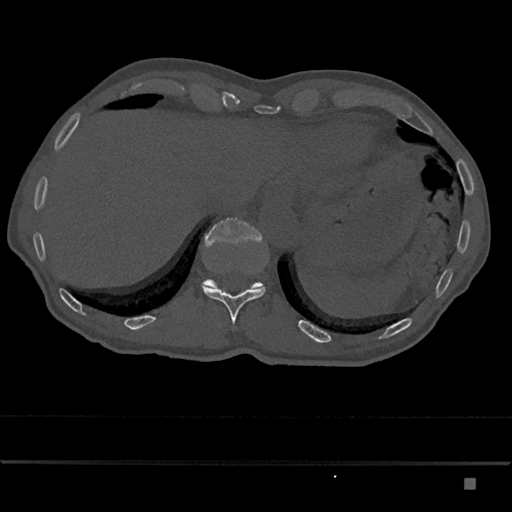
CT including the spine, one axial slice. Slice 660 of 797 in the series (ordered by position). Reconstruction kernel Br40s/3. 120 kVp. Bone window (W 1800 / L 400 HU). 0.5 mm slice thickness. 512 × 512 image matrix, field of view 390 × 390 mm. Patient: male, 72 years. From the clinical record (not read from this slice): primary cancer: prostate.
Structures marked on this image (semi-automatic segmentation, software-assisted and operator-edited):
- T11 vertebra: bounding box [x1, y1, x2, y2] px = [201, 271, 266, 324]
- T12 vertebra: [203, 218, 263, 289]